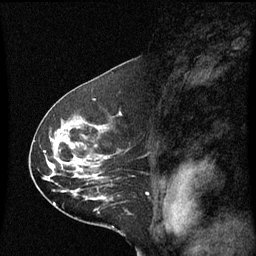
Breast MRI (dynamic contrast-enhanced), one sagittal slice. Position 37 of 60 along the scan axis. Dynamic contrast-enhanced series, image 2 of 3 at this slice position (ordered by acquisition). 1.5 T. TE 4.2 ms, TR 8.9 ms. 2 mm slice thickness. 256 × 256 image matrix. Patient: female, 53 years. Case-level facts recorded for this patient, not image findings: setting: breast cancer imaged before/during neoadjuvant chemotherapy; receptor status: HR-positive, HER2-negative.
Annotated regions visible in this slice (semi-automatically segmented with operator editing):
- analysis volume of interest (the breast-tissue region the enhancement analysis was run in; not a lesion): box from (x=32, y=100) to (x=131, y=221) px
- tumour enhancement mask (voxels above the 70 % enhancement threshold inside the analysis volume of interest): (x=48, y=158)–(x=95, y=177)